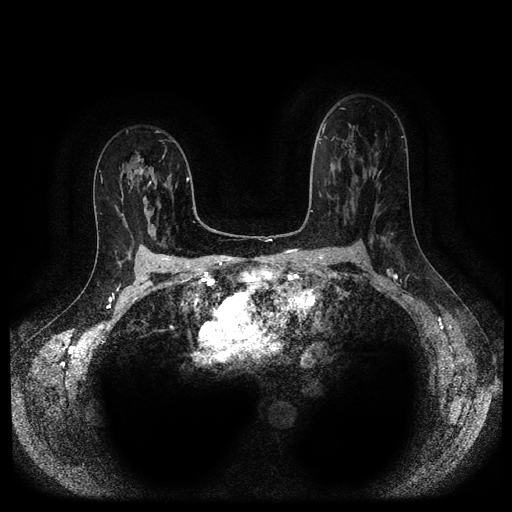
Breast MRI (dynamic contrast-enhanced, multi-phase), one axial slice. Slice 64 of 116 in the series (ordered by position). Dynamic contrast-enhanced series, time point 2 of 5 at this slice position (early post-contrast). 1.5 T. TE 2.6 ms, TR 5.3 ms. 512 × 512 image matrix. Female patient, age 50 years.
Annotated regions visible in this slice (semi-automatic segmentation, software-assisted and operator-edited):
- breast lesion (labelled 'tumour' in the annotation; benign lesions carry a separate 'benign' label): bounding box (x1, y1, x2, y2) in pixels: (131, 151, 151, 179)